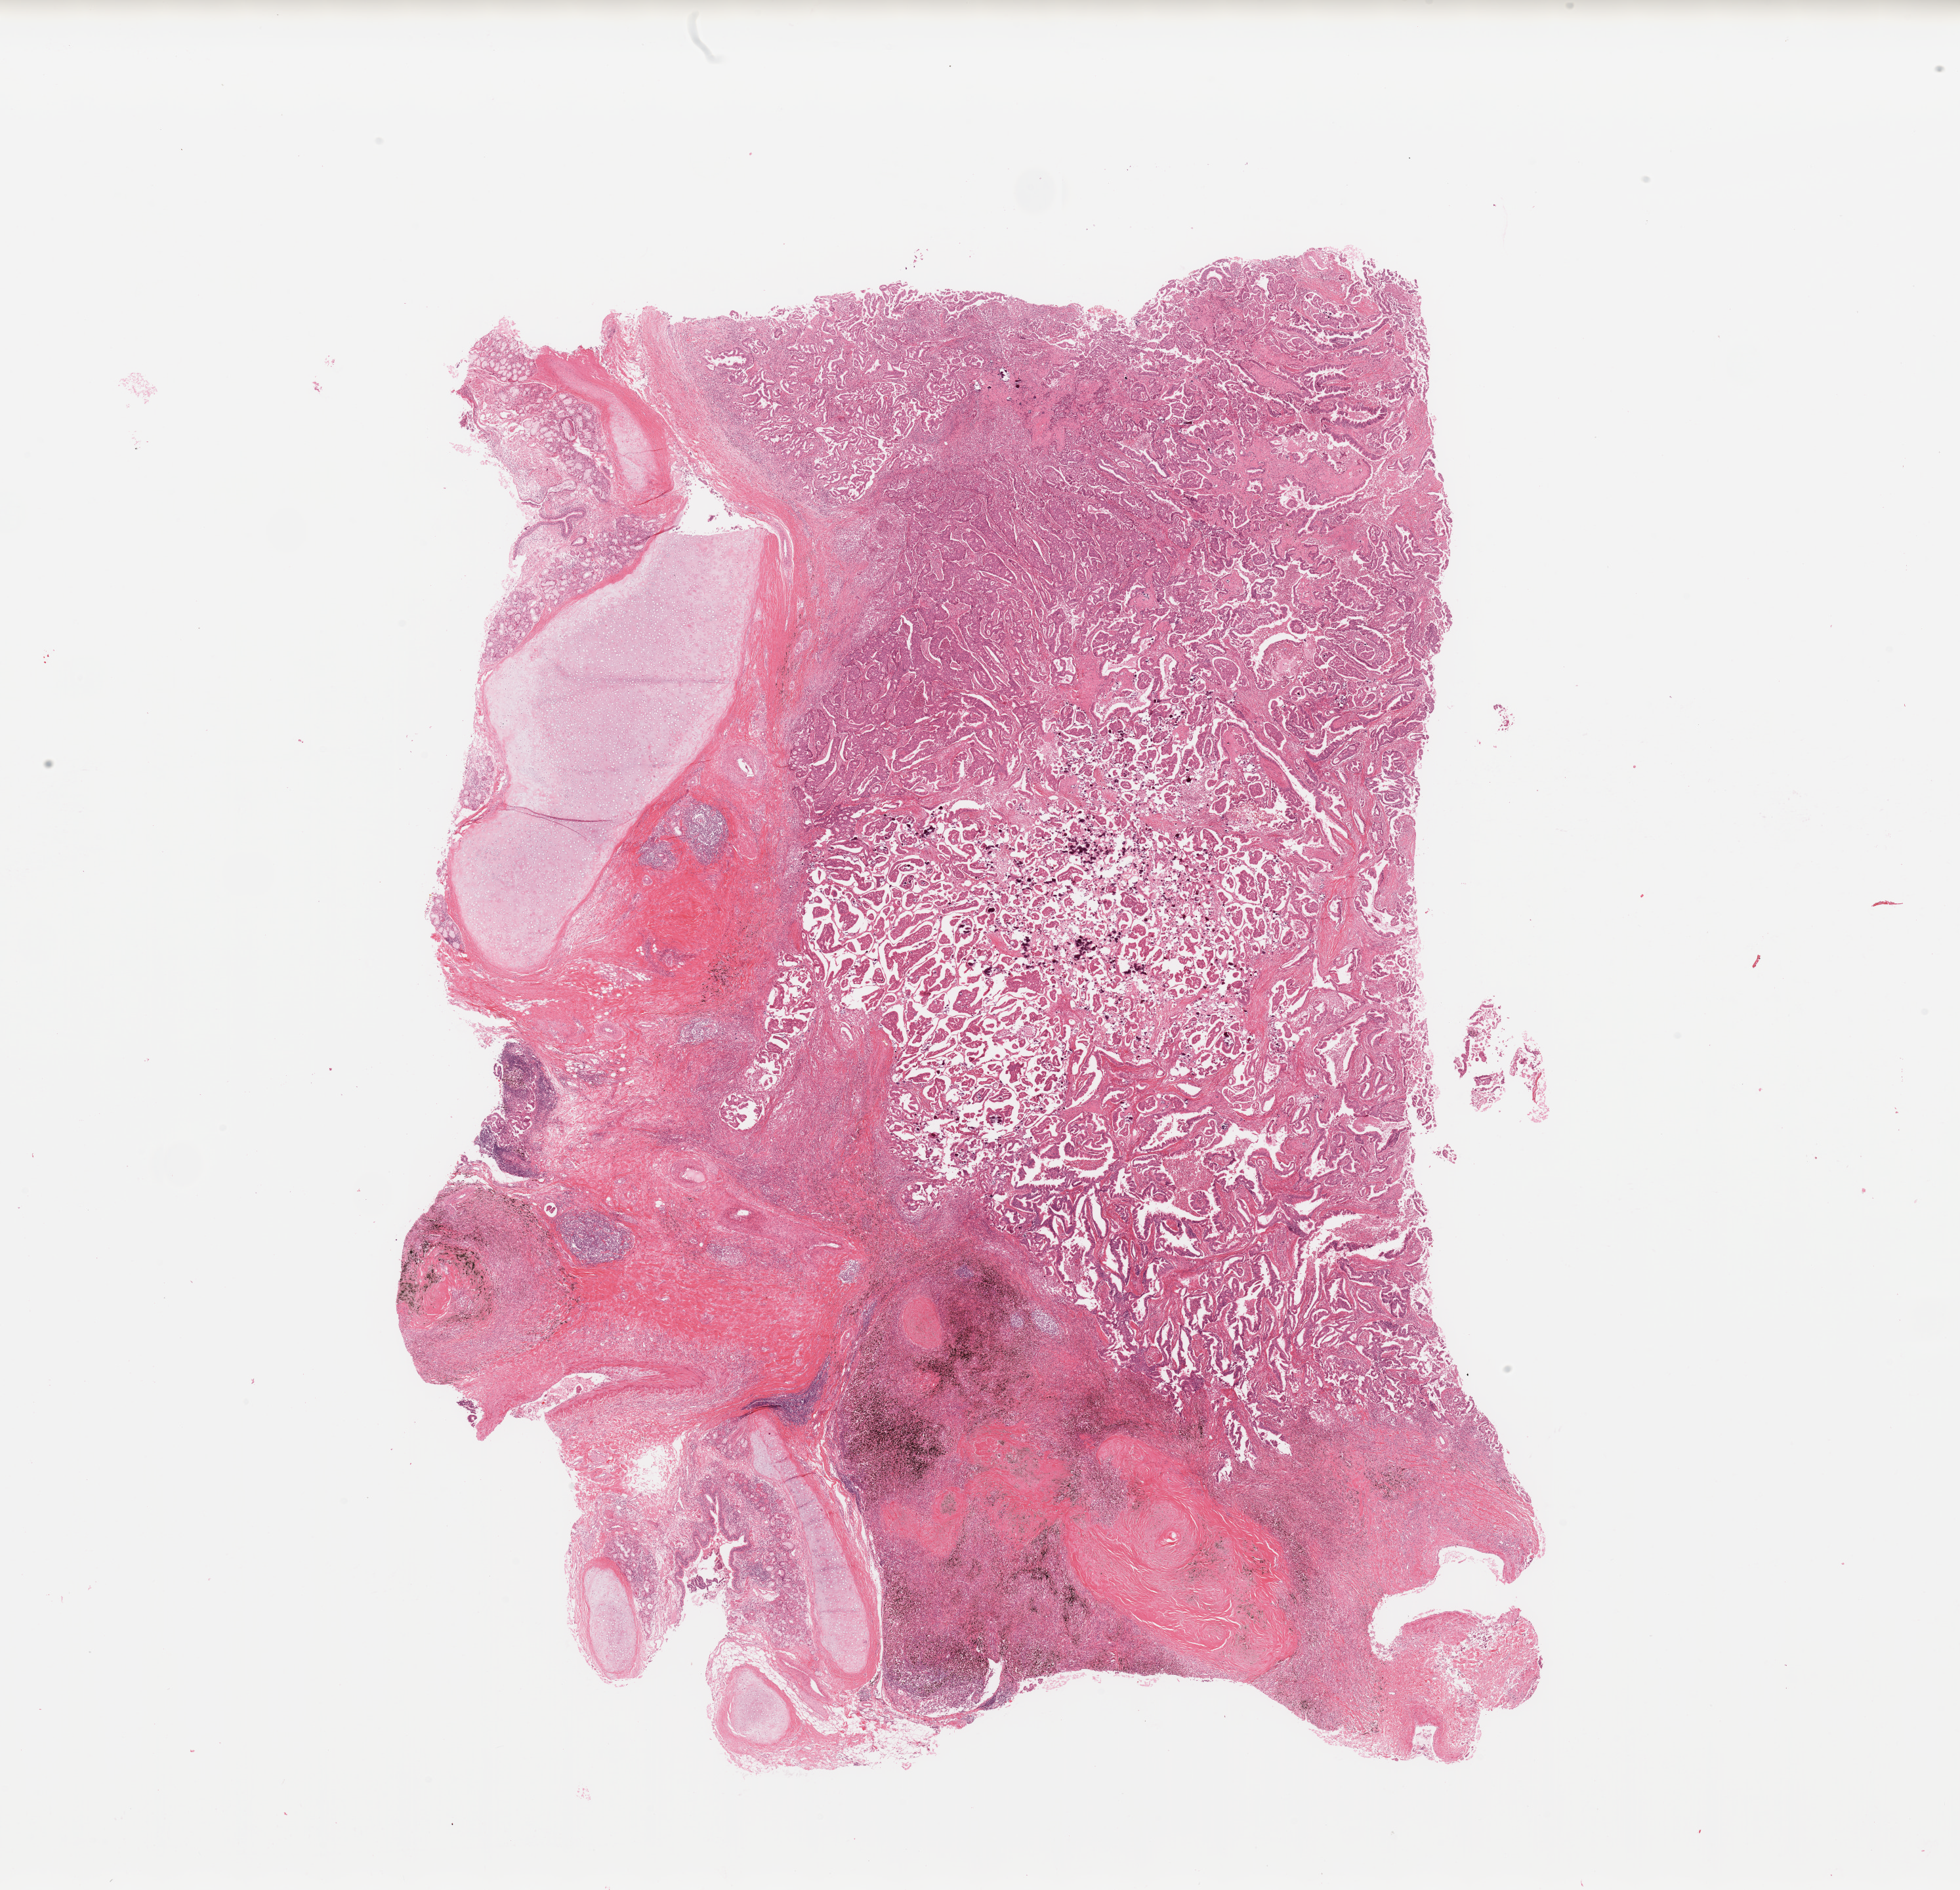
Whole-slide histology image, Hematoxylin and eosin (H&E) stained — shown as a low-resolution overview of the whole scanned area (about 23.6 x 22.8 mm, slide scanned at 20x); lung, tumour tissue. 67-year-old male patient. Histologic grade: G2 (moderately differentiated).
Diagnosis: Adenocarcinoma, NOS. AJCC pathologic stage: IIIA.